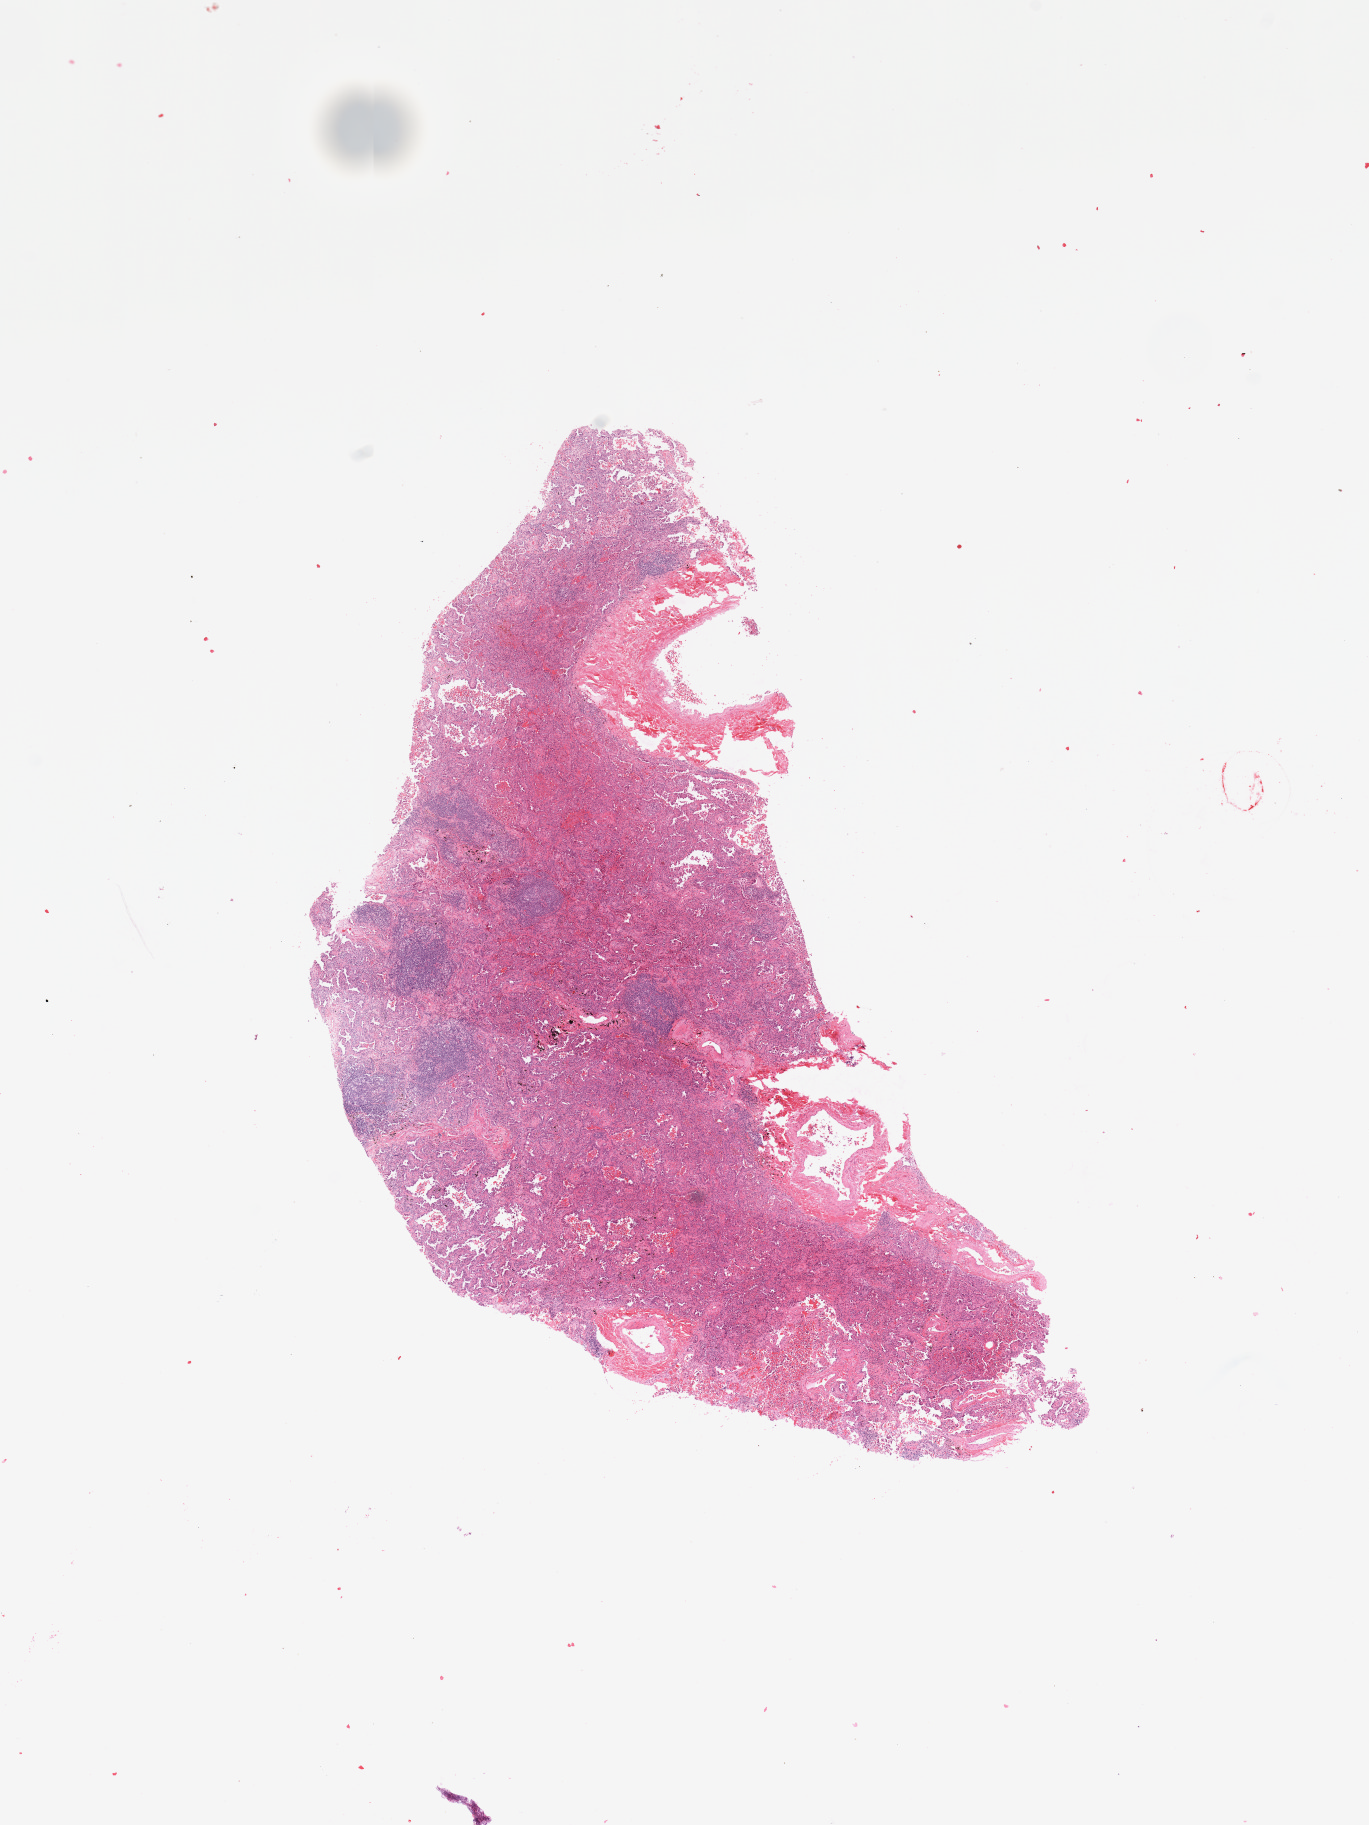
Whole-slide histology image, H&E — low-resolution overview of the scanned area, about 10.8 x 14.4 mm; tumour tissue sample, sampled site: lung. 70-year-old female patient. Histologic grade: G2 (moderately differentiated). Slide review estimates, as recorded: tumour nuclei 75%, necrosis 0%.
AJCC pathologic stage: IIIA. Histologic diagnosis: Adenocarcinoma, NOS.